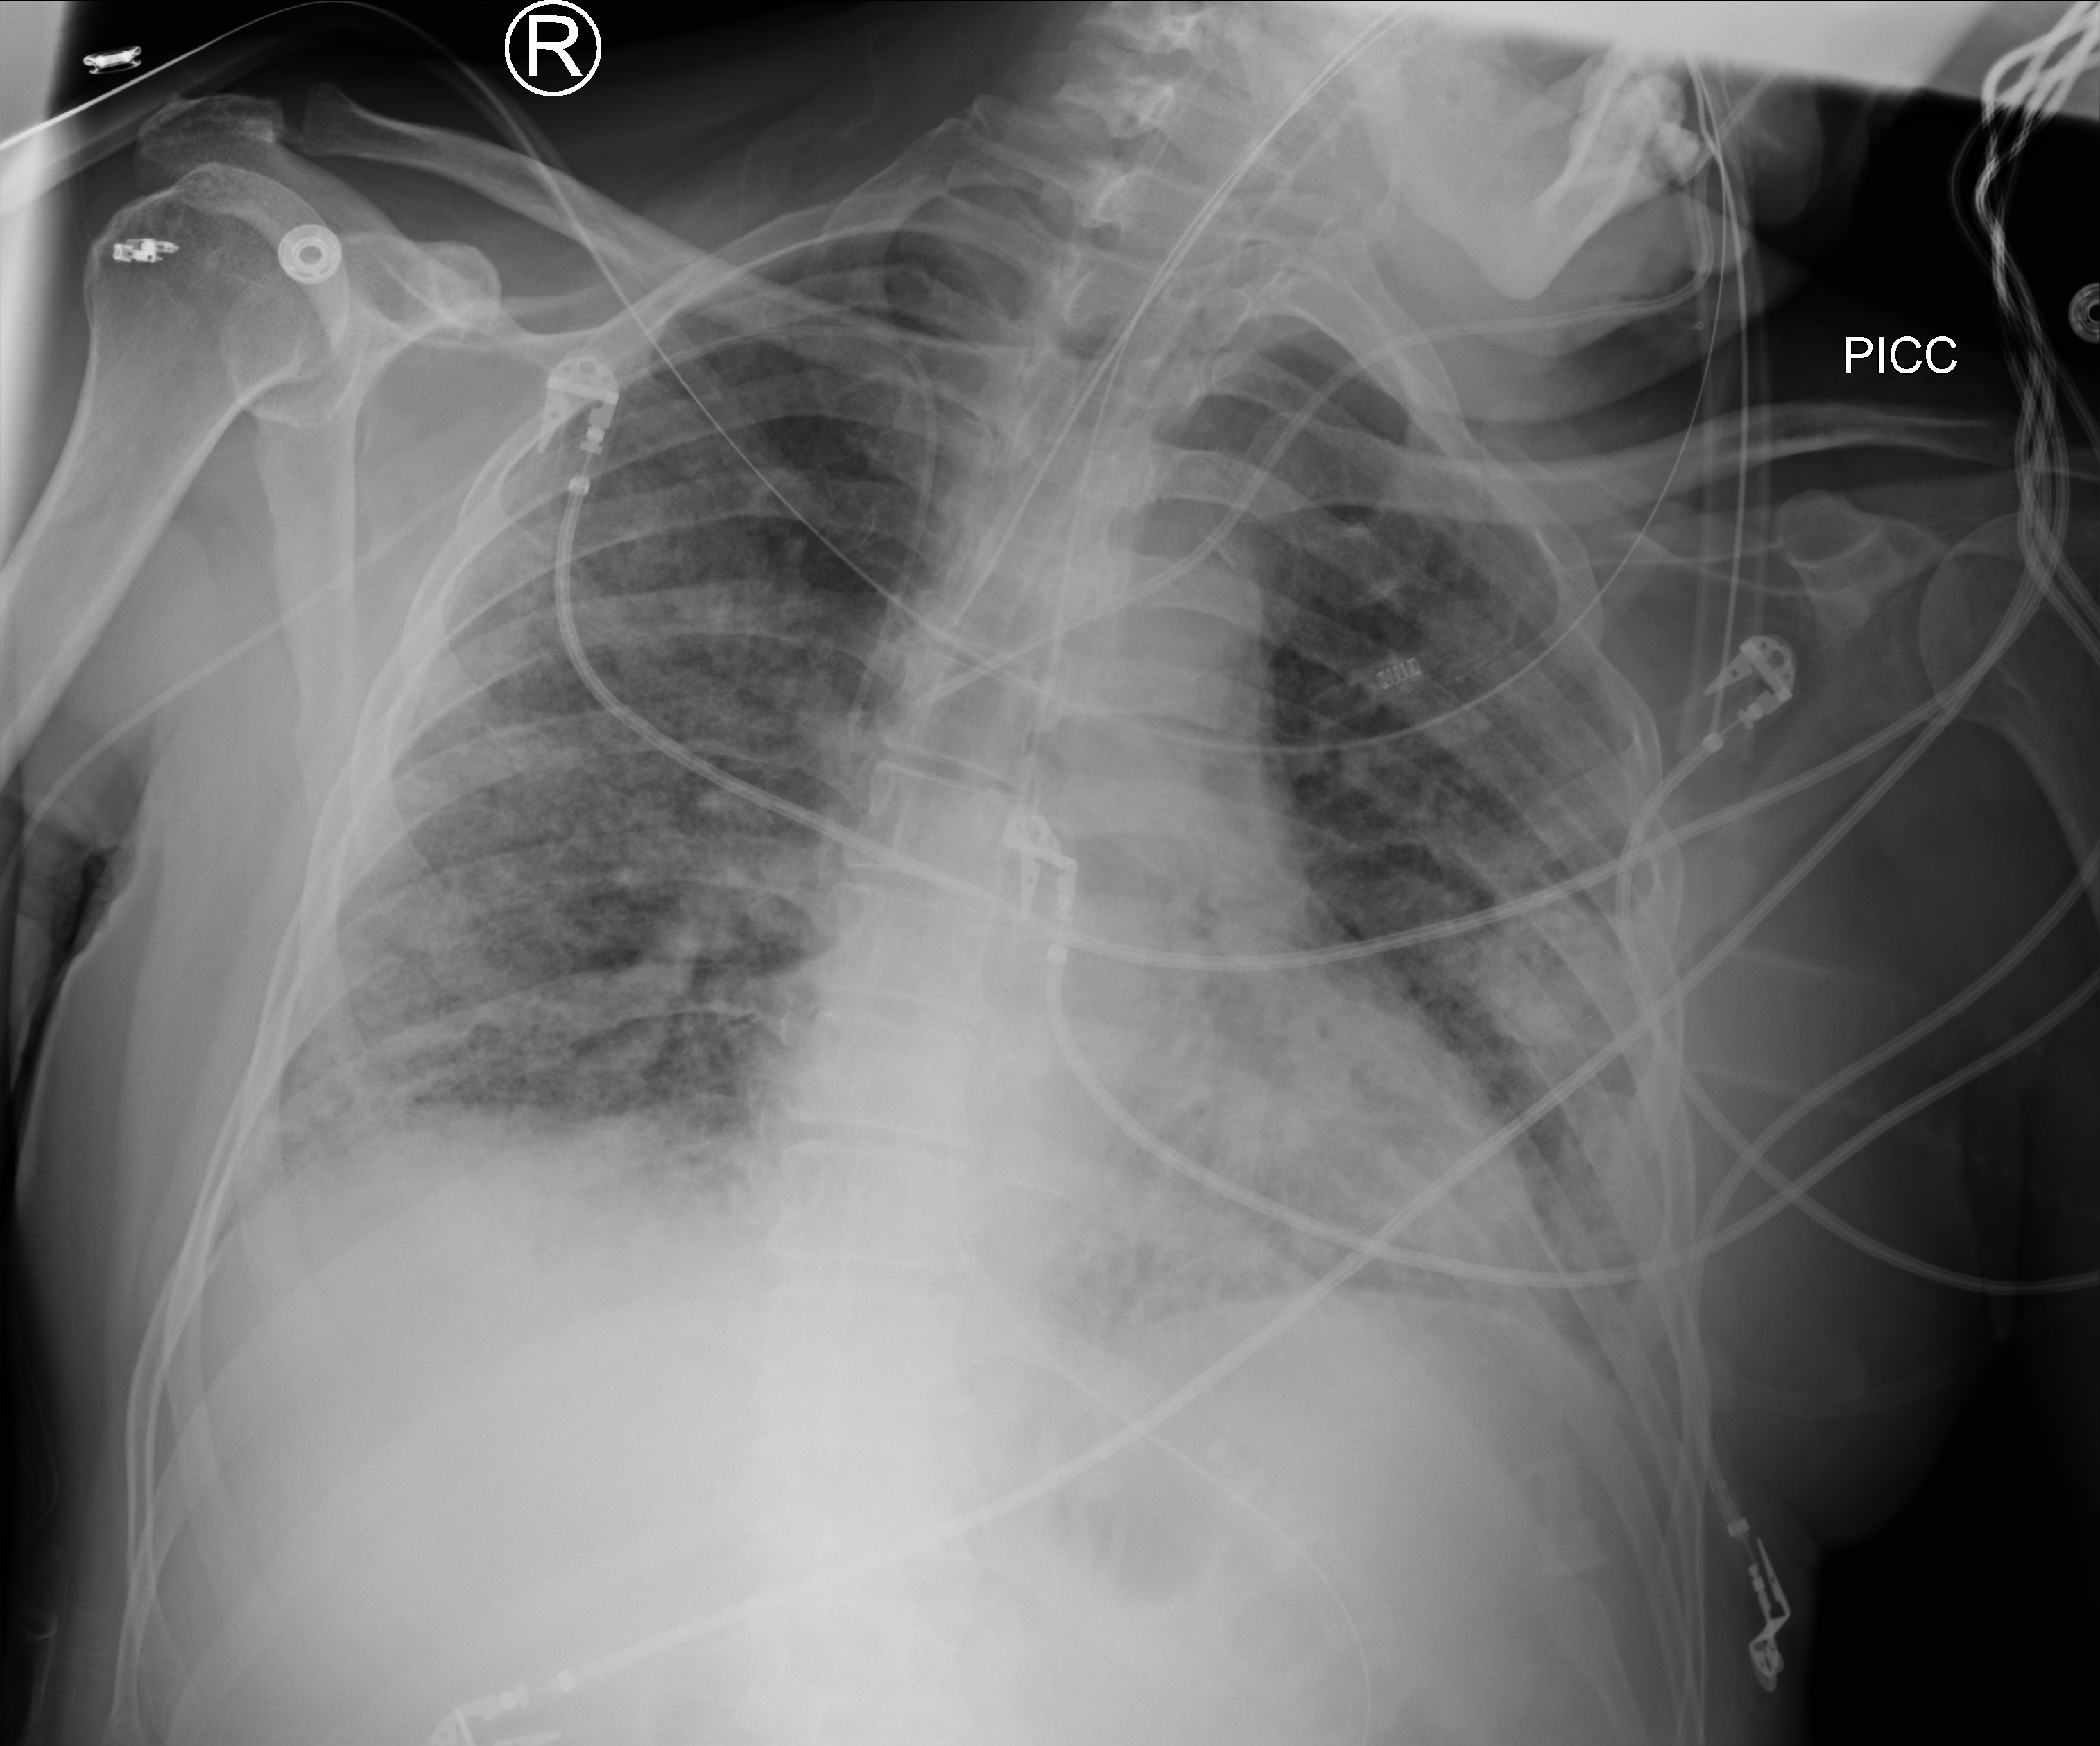
Bedside chest radiograph (computed radiography), anteroposterior (AP) projection. Patient hospitalised with COVID-19; male, aged 60–74 years.
Hospital-stay facts (about this admission, not read from this image; timing relative to this image not recorded): diabetes (admission record): no.